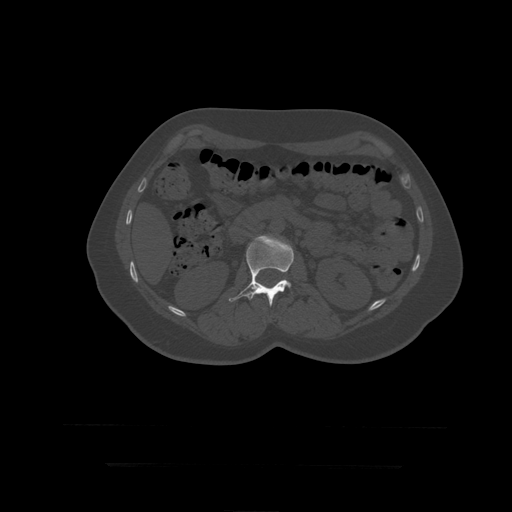
CT including the spine, one axial slice; slice 148 of 399 in the series (ordered by position); bone window (W 1800 / L 400 HU); 1.25 mm slice thickness; 512 × 512 image matrix, field of view 450 × 450 mm. Patient age 41 years. From the clinical record (not read from this slice): primary cancer: breast.
Structures marked on this image (semi-automatic segmentation, software-assisted and operator-edited):
- L2 vertebra: bounding box (x1, y1, x2, y2) in pixels: (229, 235, 294, 307)